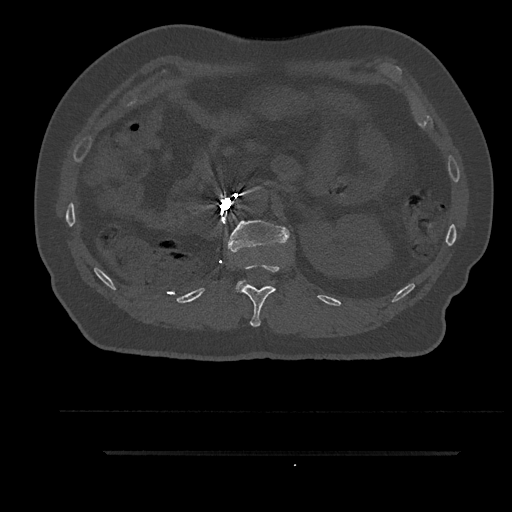
CT including the spine, one axial slice; slice 213 of 797 in the series (ordered by position); reconstruction kernel Br40s/3; bone window (W 1800 / L 400 HU); 0.5 mm slice thickness; 512 × 512 image matrix, field of view 432 × 432 mm. Male patient, age 63 years. Case-level facts recorded for this patient, not image findings: primary cancer: renal; vertebrae with lytic lesions (as recorded): T8.
Outlined on this slice (semi-automatic segmentation, software-assisted and operator-edited):
- L1 vertebra: bounding box (x1, y1, x2, y2) in pixels: (228, 220, 290, 292)
- T12 vertebra: (238, 264, 282, 327)